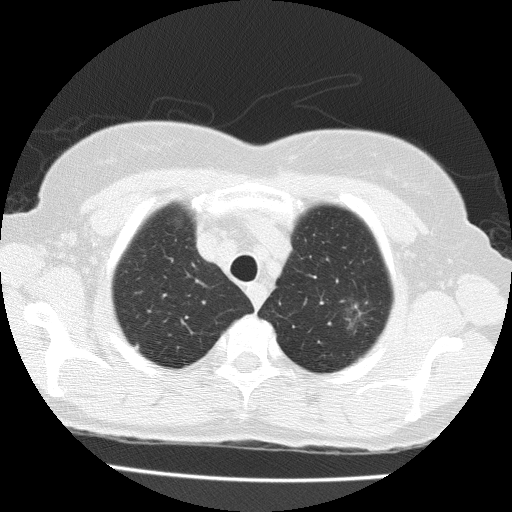
Chest CT (low-dose screening protocol), one axial image, baseline annual screen, lung window (W 1500 / L -600 HU), 2 mm slice thickness, slice 29 of 183 in the series, 512 × 512 image matrix. Female, age 71 years at enrolment. Former smoker at enrolment.
Expert-annotated lung lesion, bounding box <335,289,392,340> (left, top, right, bottom; pixels). Reader record for this screening exam (exam-level; its link to the box is not recorded): non-calcified nodule or mass ≥4 mm, left upper lobe, 15 × 10 mm, spiculated (stellate) margins, soft tissue attenuation. Official screen result: positive, change unspecified: nodule(s) >= 4 mm or enlarging nodule(s), mass(es), or other non-specific abnormalities suspicious for lung cancer. Later outcome: lung cancer diagnosed 49 days after this screen — adenocarcinoma with mixed subtypes, left upper lobe, well differentiated (G1), stage IA (AJCC 6th edition), 15 mm at pathology.